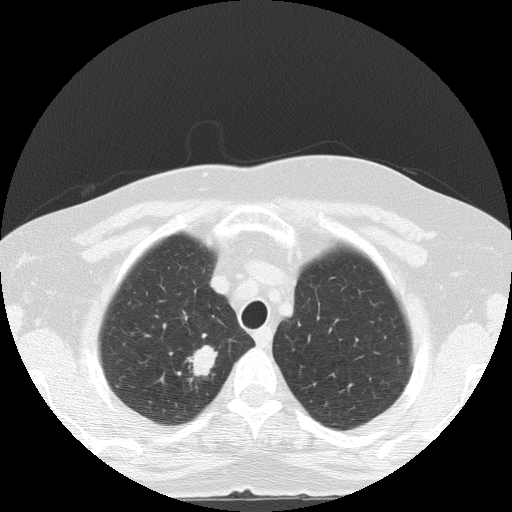
Low-dose screening chest CT, one axial slice. Slice 112 of 133 in the series (ordered by position). Lung window (W 1500 / L -600 HU). 512 × 512 image matrix.
Structures marked on this image (expert manual segmentation):
- lesion 1 (tumor, upper lobe of right lung): bounding box <187,345,218,377> (left, top, right, bottom; pixels)